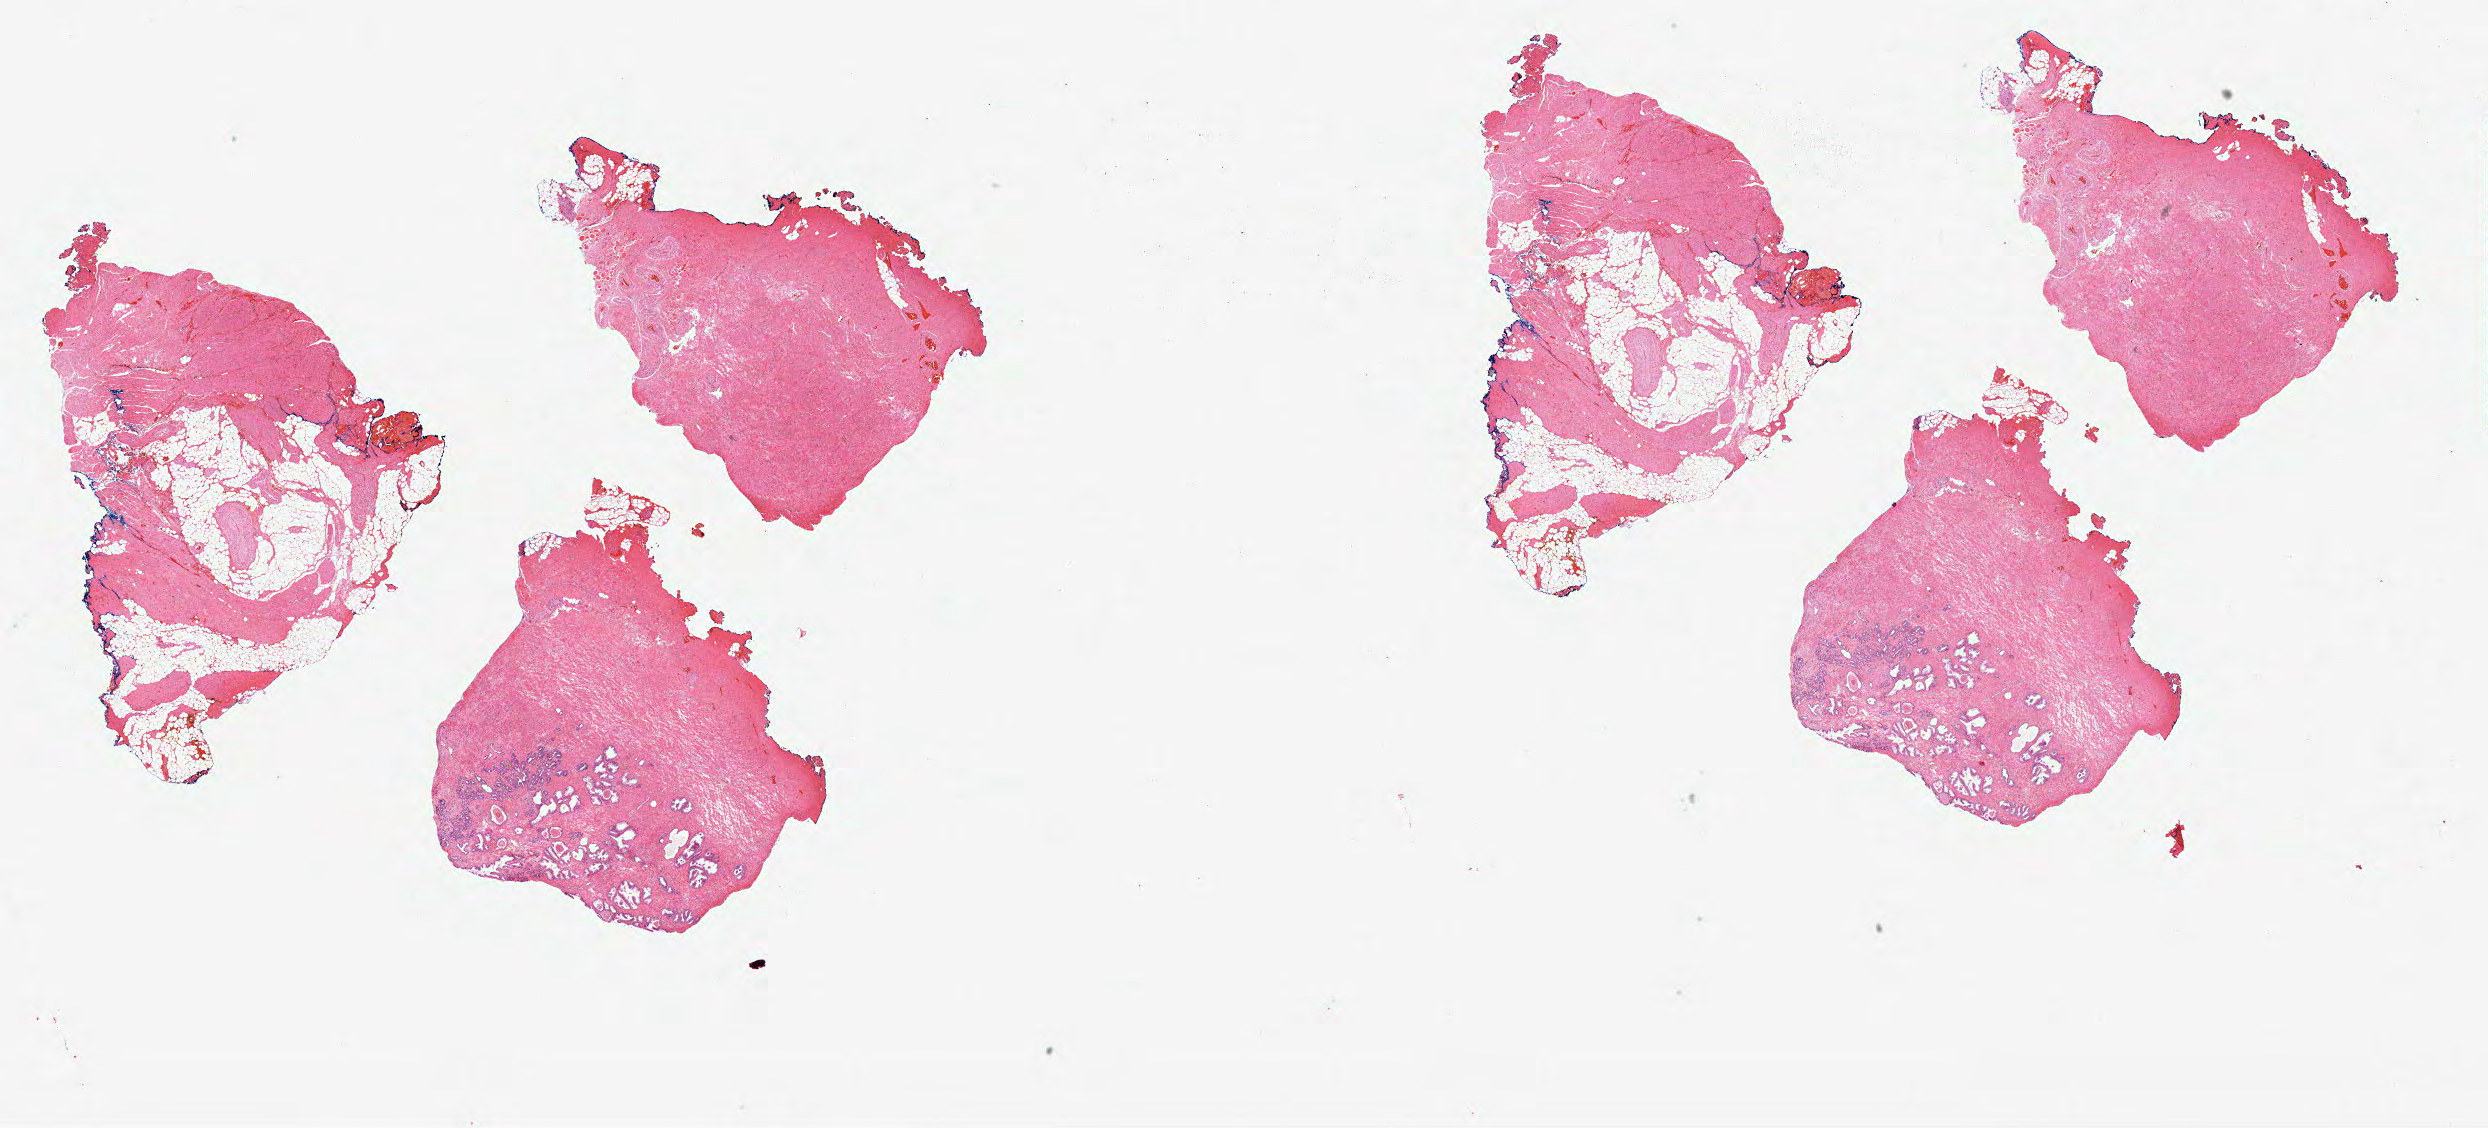
Whole-slide histology image, H&E, a low-resolution overview of the entire scanned area, about 40.1 x 18.2 mm (slide scanned at 40x), formalin-fixed paraffin-embedded (FFPE) diagnostic section, sample: primary tumour, prostate. Male patient; age at initial diagnosis 61 years. Gleason score: 7 (3+4).
Pathologic diagnosis: Acinar cell carcinoma (prostate gland). Laterality: bilateral. Lymph nodes positive (case pathology): 0 of 6 examined.